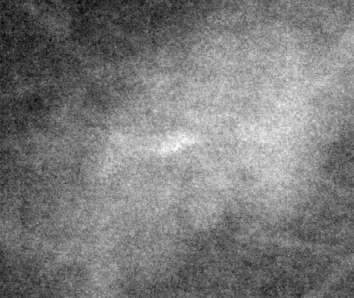
Crop from a digitized film mammogram around one marked abnormality; right breast; CC view.
- Finding: mass, shape lobulated / irregular, margins ill defined; BI-RADS assessment category 4; subtlety rating 4 on a 1 (subtle) to 5 (obvious) scale; pathology (as recorded): benign.